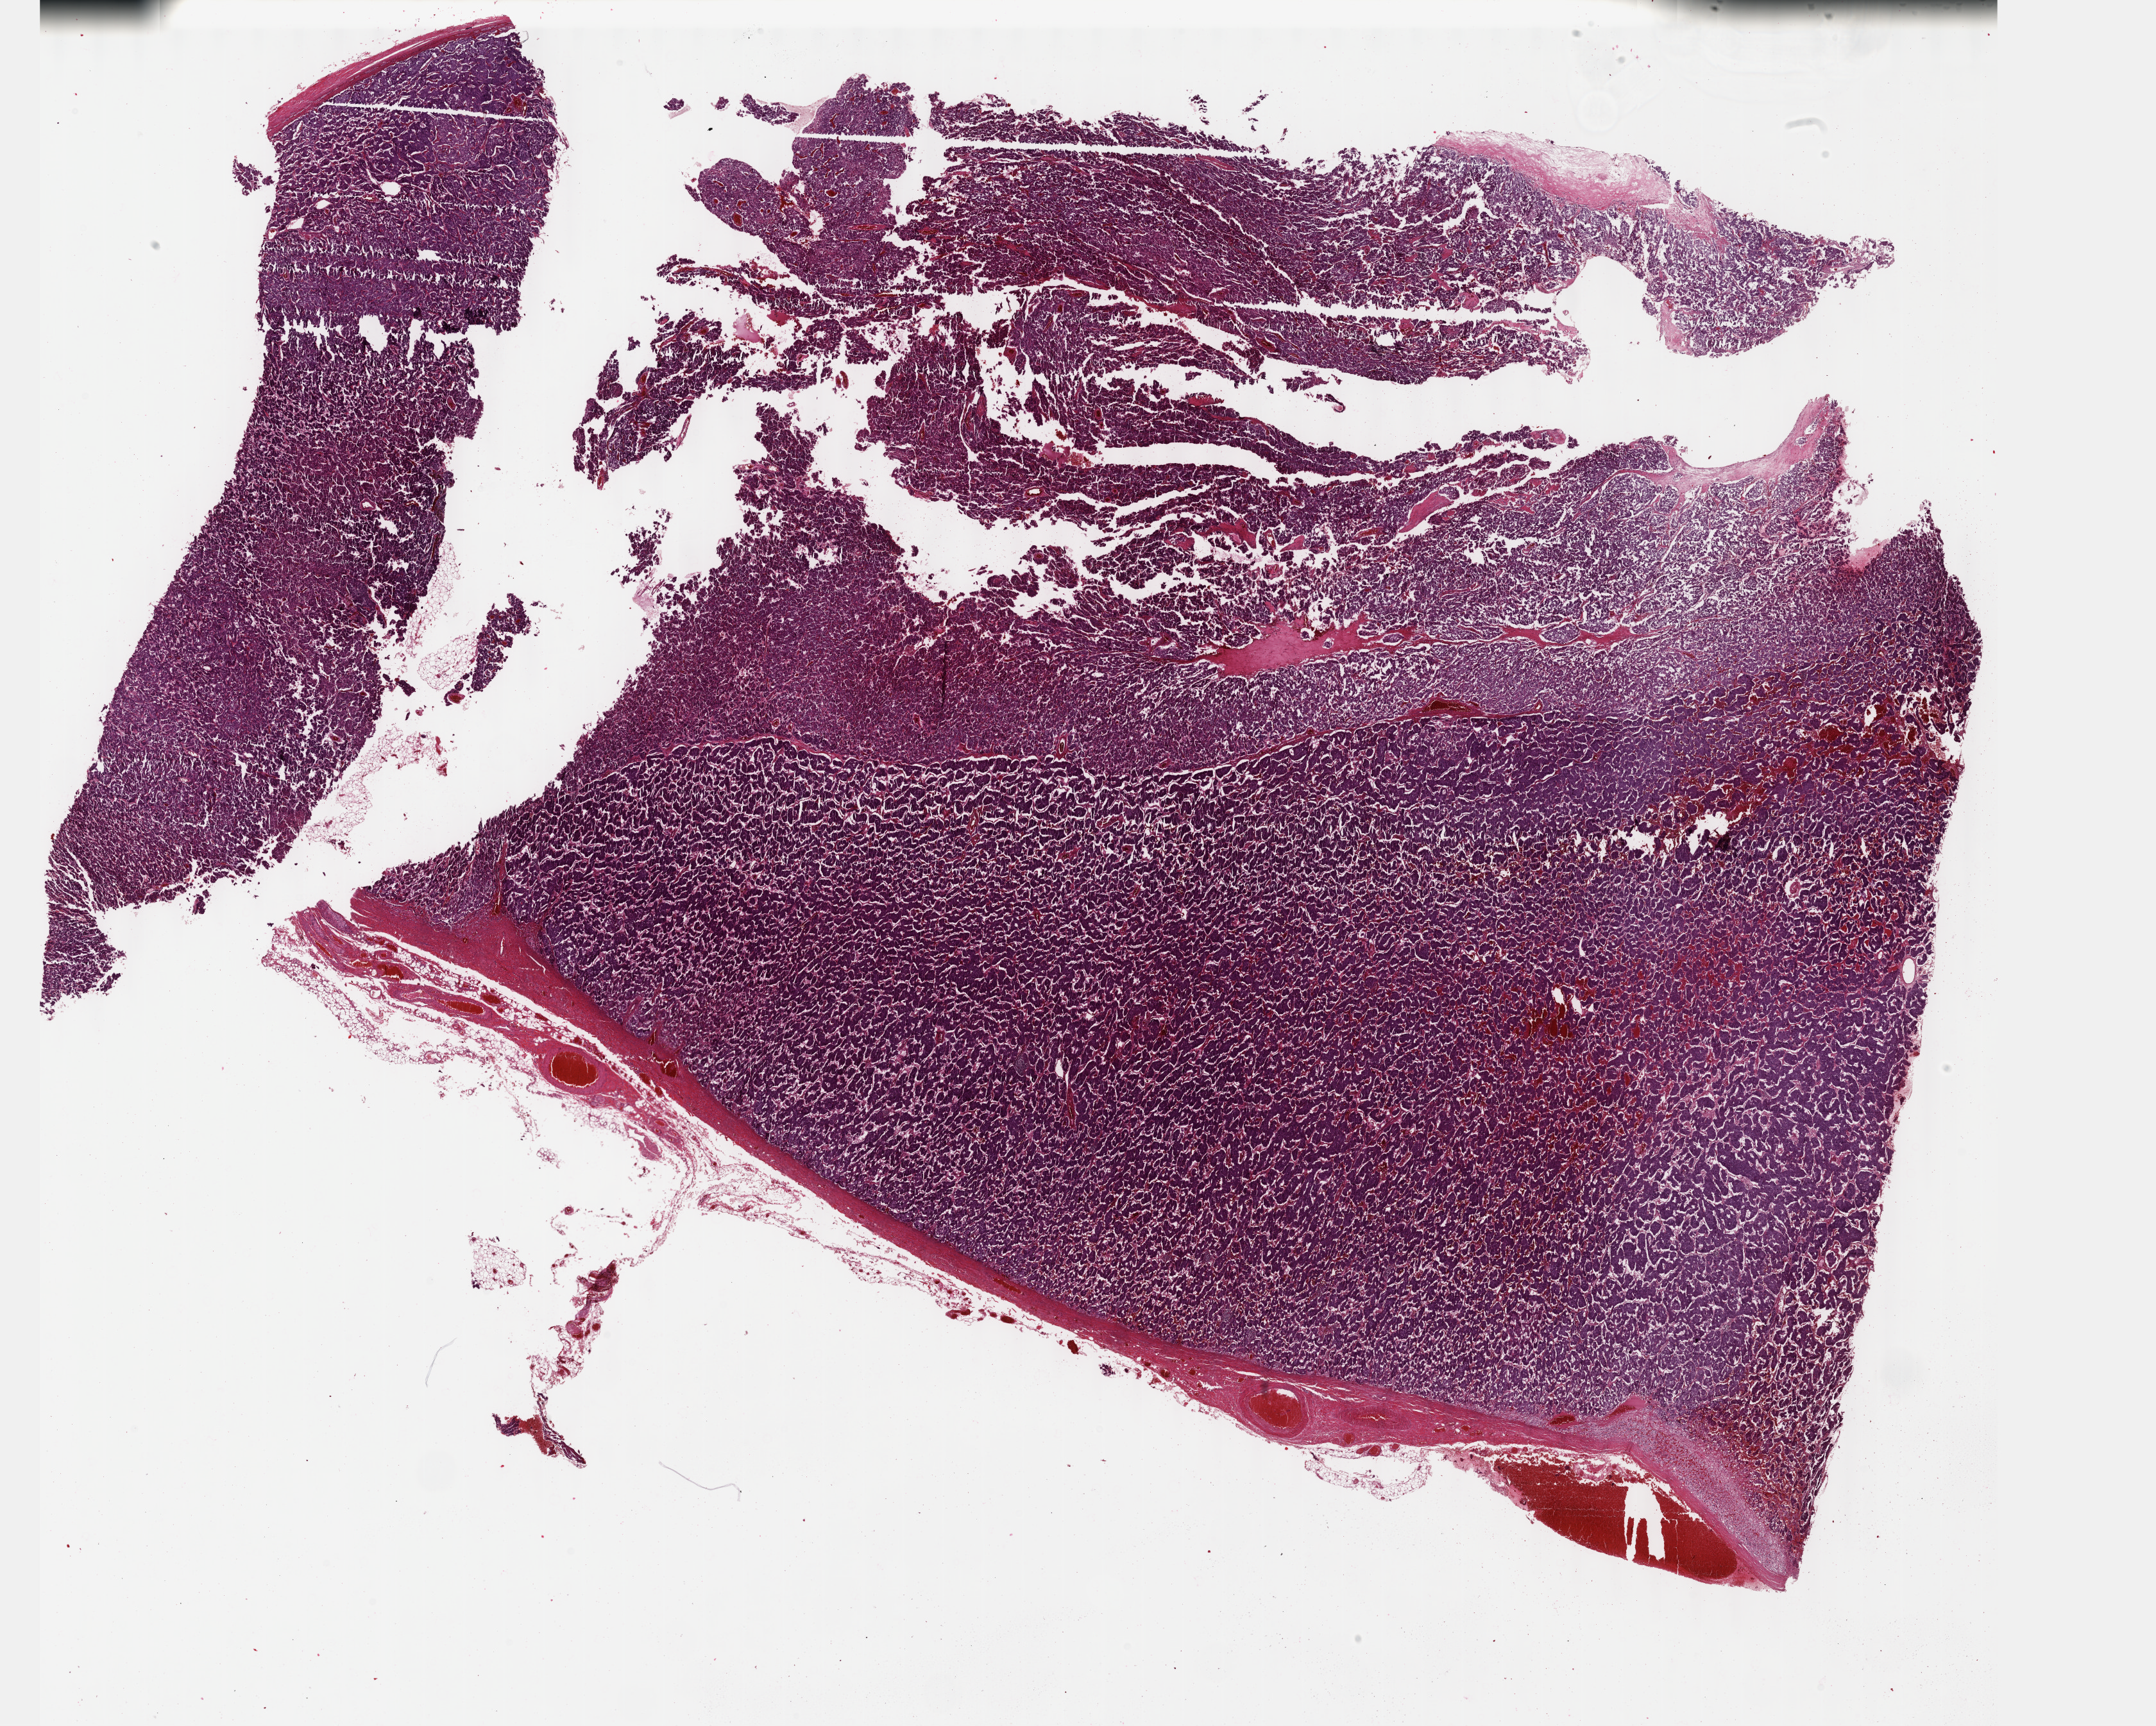
Whole-slide histology image, H&E-stained — whole scanned area (about 27.2 x 21.7 mm) shown as a low-resolution overview; formalin-fixed paraffin-embedded (FFPE) diagnostic section; adrenal gland, primary tumour sample. Patient: male, age at initial diagnosis 36 years.
- pathologic diagnosis: Pheochromocytoma, malignant